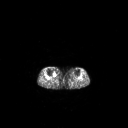
FDG PET of an extremity soft-tissue mass (from a PET/CT study), one axial slice. 3.27 mm slice thickness. 128 × 128 image matrix, field of view 700 × 700 mm. Female patient, age 65 years. Case-level facts recorded for this patient, not image findings: histological type: undifferentiated – high grade; grade: high; site of the primary tumour: right thigh.
Outlined on this slice (expert contour drawn on MRI and transferred to this co-registered scan by the dataset authors):
- gross tumour volume (mass): bounding box (x1, y1, x2, y2) in pixels: (53, 72, 56, 77)